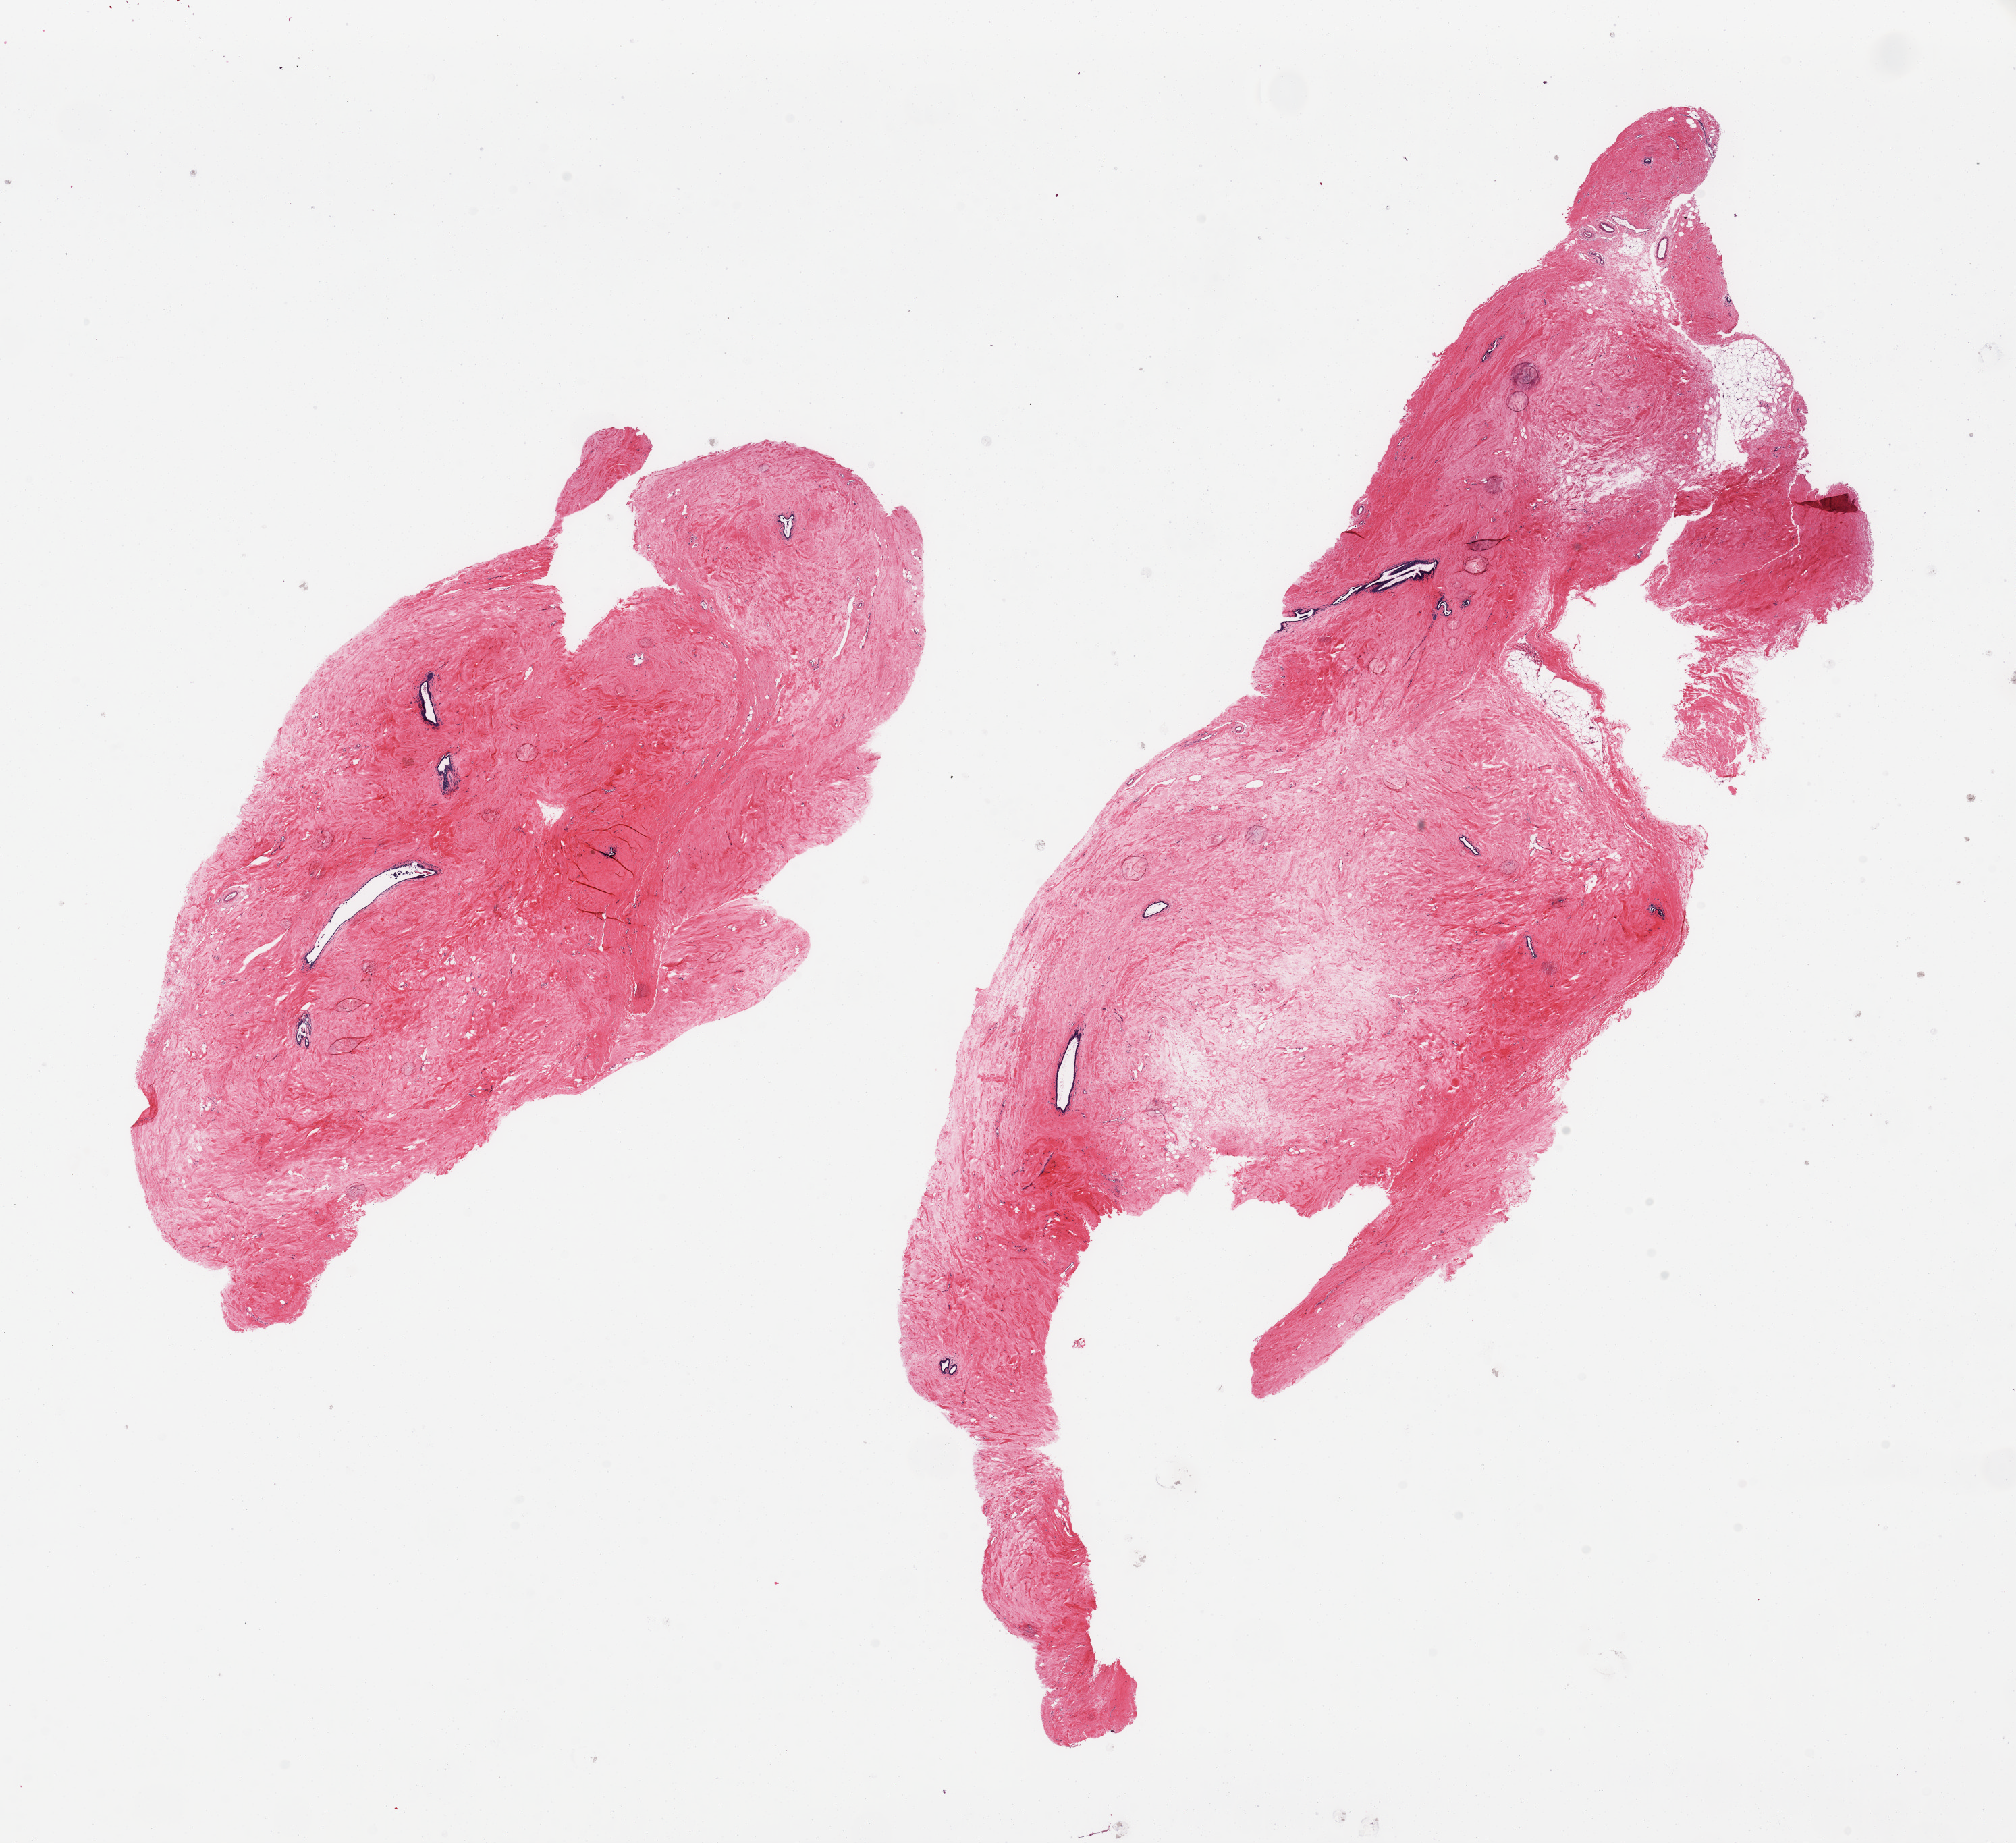
Haematoxylin and eosin whole-slide image — low-resolution overview of the scanned area, about 23.6 x 21.6 mm, PAXgene-fixed paraffin-embedded (PFPE) section, section of breast (target tissue), tissue donor sample.
* reviewer comment on this tissue sample: 2 pieces, gynecomastoid stromal and focal ductal hyperplasia